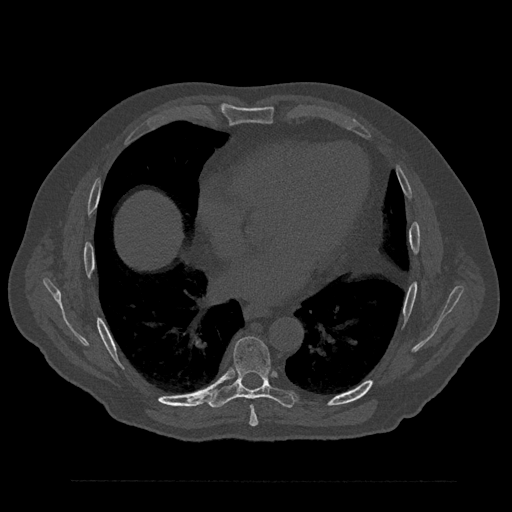
CT including the spine, one axial slice; bone window (W 1800 / L 400 HU); 0.5 mm slice thickness; 512 × 512 image matrix, field of view 430 × 430 mm. Patient: male, 61 years. From the clinical record (not read from this slice): primary cancer: prostate.
Annotated regions visible in this slice (semi-automatic segmentation, software-assisted and operator-edited):
- T7 vertebra: box from (x=249, y=405) to (x=258, y=426) px
- T8 vertebra: (x=208, y=336)–(x=296, y=409)